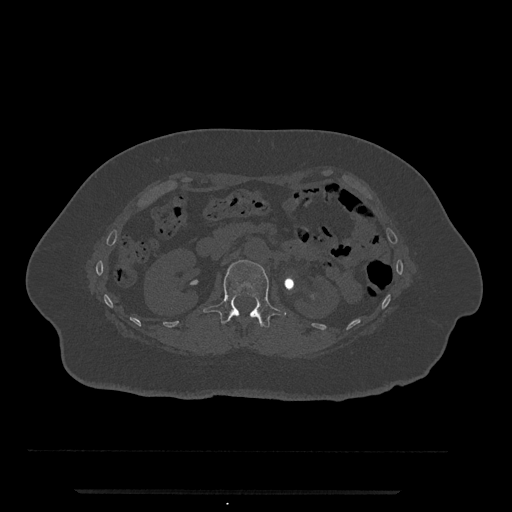
CT including the spine, one axial slice; slice 110 of 797 in the series (ordered by position); reconstruction kernel Br40s/3; bone window (W 1800 / L 400 HU); 0.5 mm slice thickness; 512 × 512 image matrix, field of view 440 × 440 mm. Female patient, age 51 years. From the clinical record (not read from this slice): primary cancer: neuro.
Structures marked on this image (semi-automatically segmented with operator editing):
- L1 vertebra: bounding box [x1, y1, x2, y2] px = [203, 260, 286, 328]
- T12 vertebra: [257, 322, 260, 324]